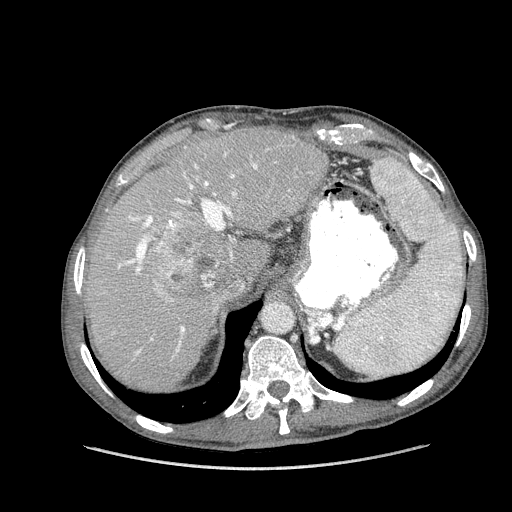
Contrast-enhanced abdominal CT (liver protocol), one axial slice. Position 109 of 162 along the scan axis. Reconstruction kernel STANDARD. 100 kVp. Soft-tissue window (W 400 / L 40 HU). 2.5 mm slice thickness. 512 × 512 image matrix. Case-level facts recorded for this patient, not image findings: diagnosis: hepatocellular carcinoma (patient treated with transarterial chemoembolisation; whether this scan precedes or follows treatment is not stated here); TNM stage (as recorded): Stage-IIIA; Child-Pugh class: A; tumour nodularity: multinodular.
Outlined on this slice (semi-automatically segmented with operator editing):
- liver parenchyma outside the tumour (the mass and vessels are separate outlines, so this box may not span the whole liver): box from (x=86, y=126) to (x=328, y=390) px
- mass: (x=153, y=213)–(x=231, y=297)
- liver vessels: (x=118, y=153)–(x=257, y=355)